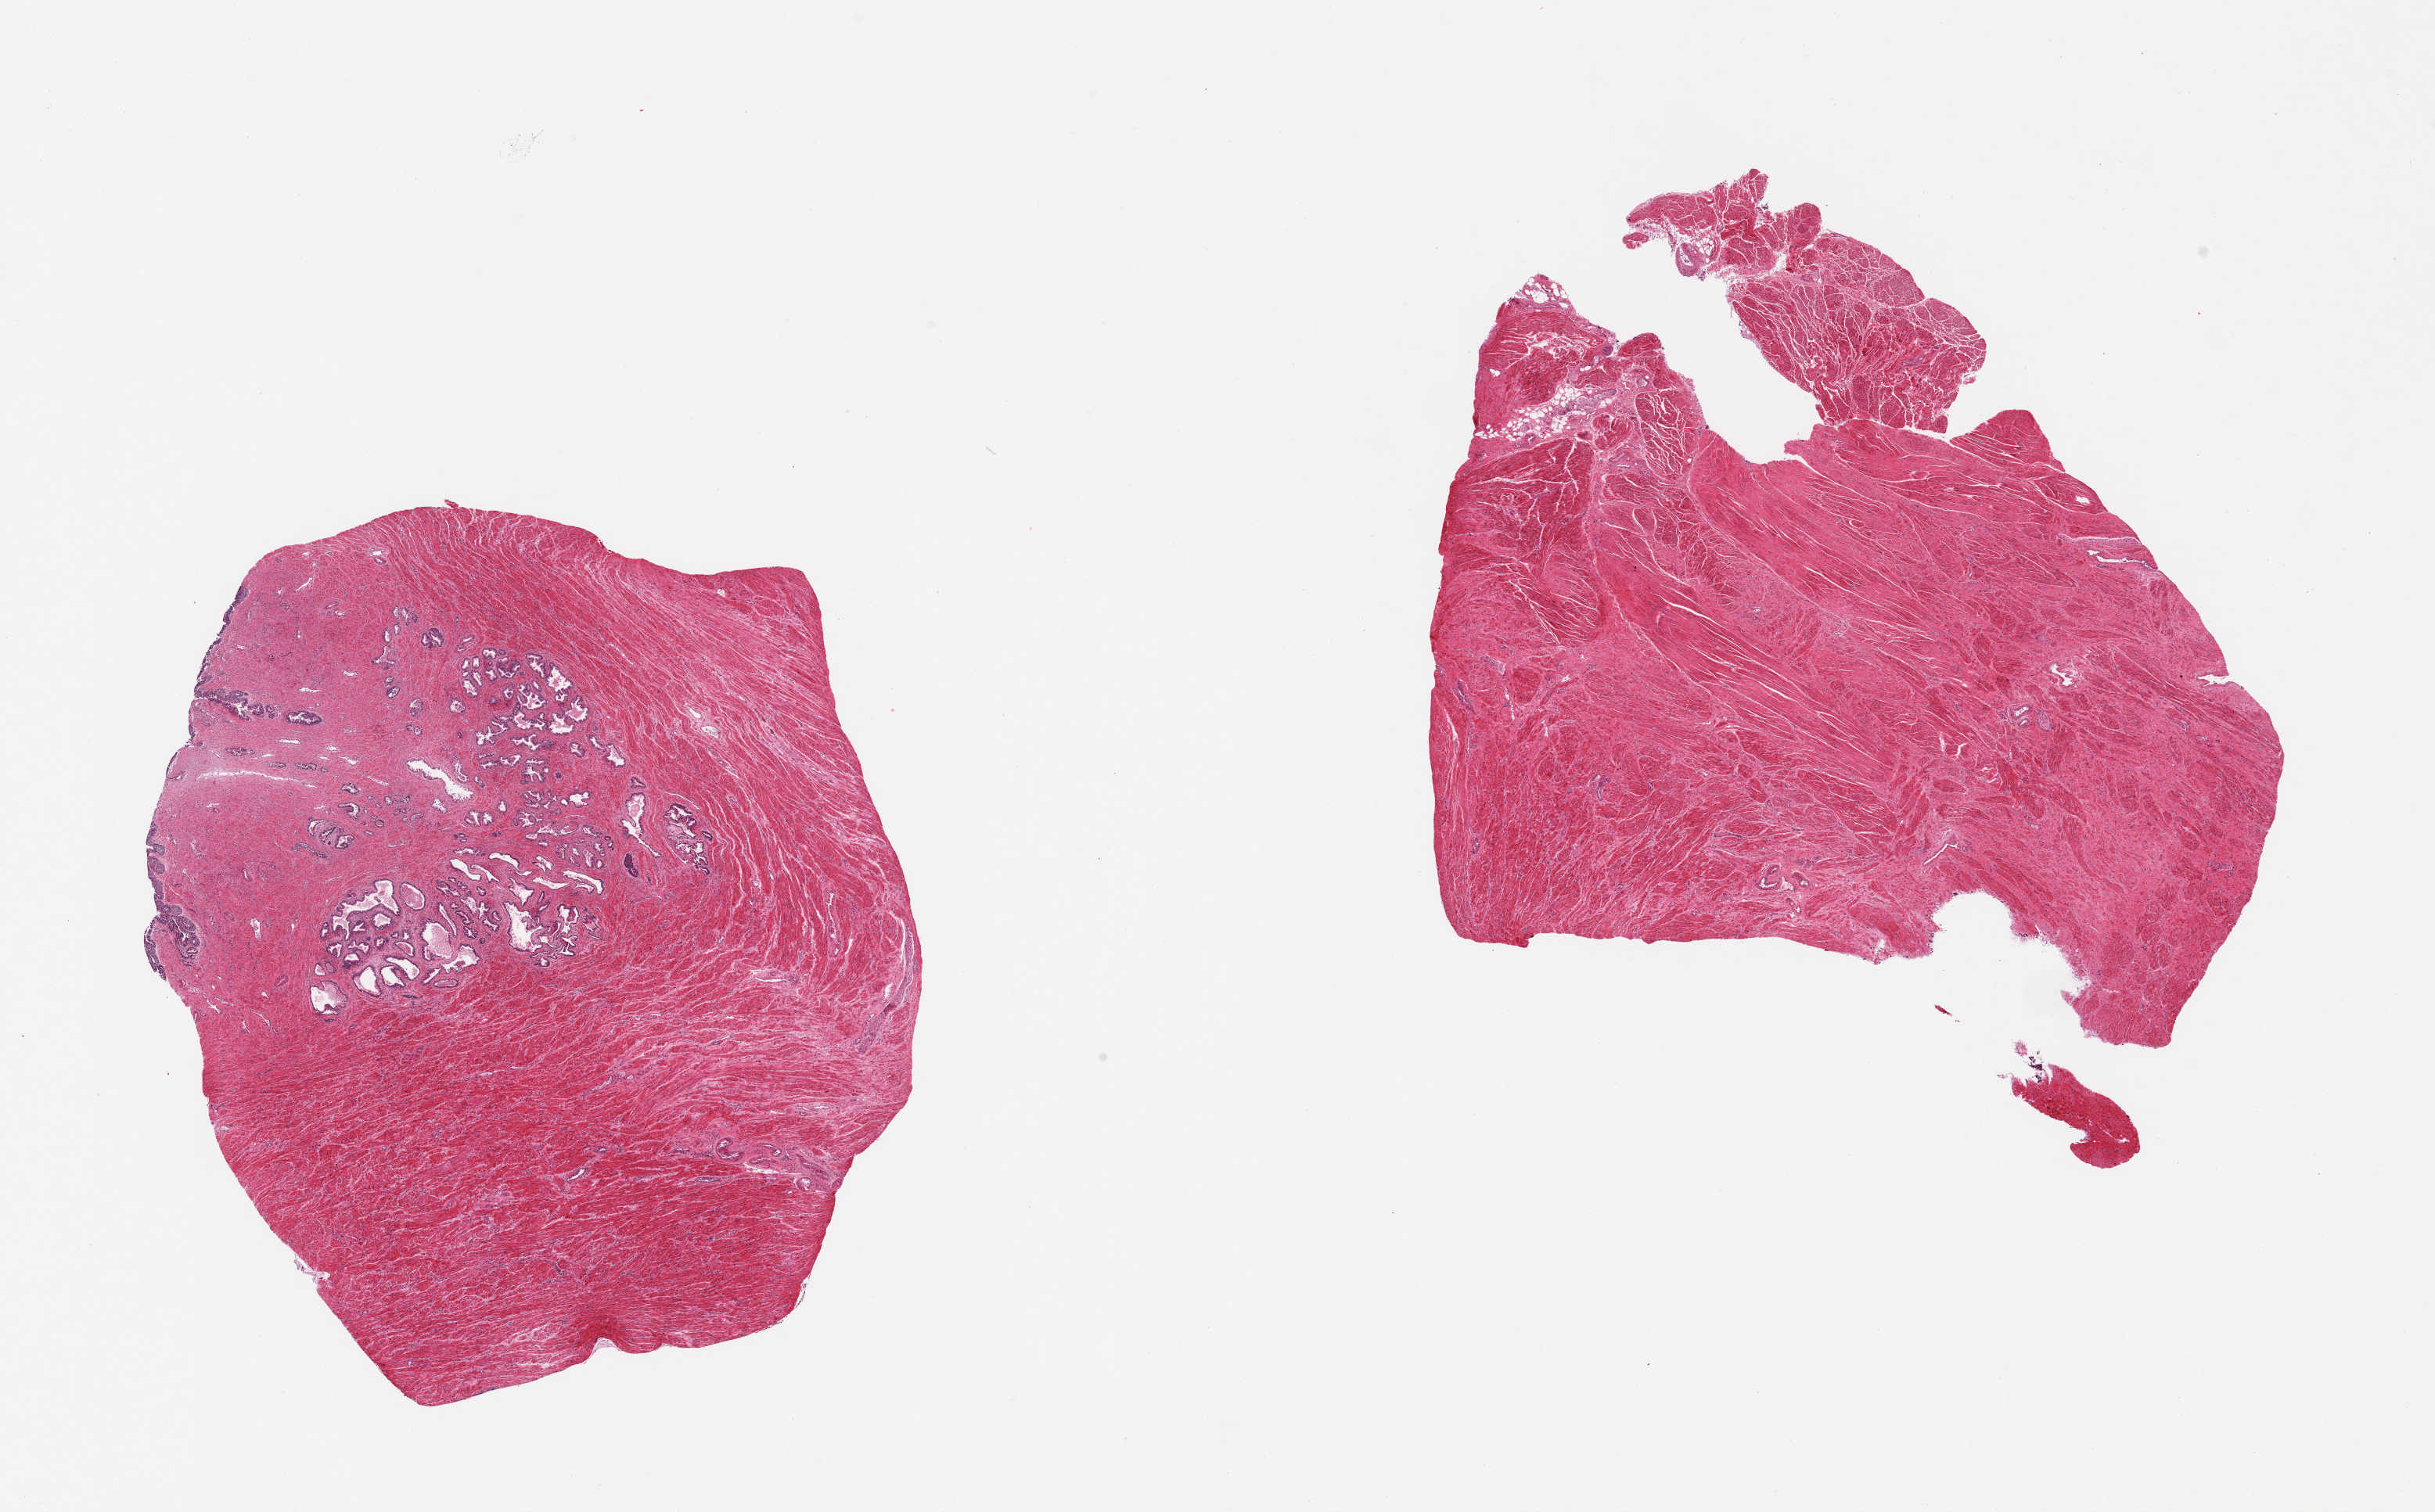
Hematoxylin and eosin (H&E) whole-slide image, brightfield — low-resolution overview of the scanned area, about 24.6 x 15.3 mm; PAXgene-fixed paraffin-embedded (PFPE) section; sampled site (target tissue): prostate; tissue donor sample. Male donor.
Pathologist's review note for this sample: 2 pieces, glandular & stromal hyperplasia; stroma predominates.